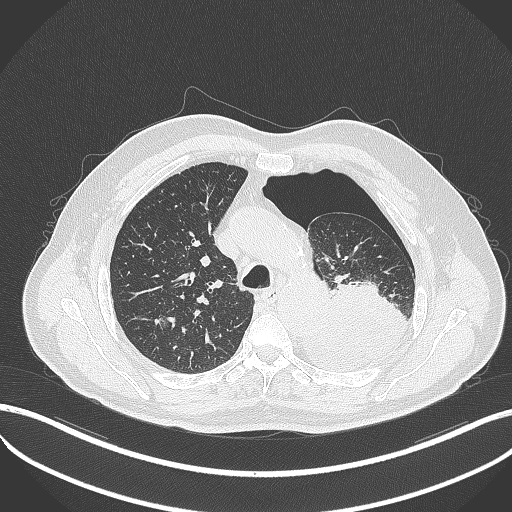
Chest CT, one axial slice. Slice 369 of 464 in the series (ordered by position). 120 kVp. Lung window (W 1500 / L -600 HU). 1 mm slice thickness. 512 × 512 image matrix, field of view 400 × 400 mm. Male patient, age 76 years. From the clinical record (not read from this slice): clinical TNM (as recorded): T3 N0 M1b.
Annotated regions visible in this slice (bounding box drawn by a radiologist):
- lung tumour (recorded histology: adenocarcinoma): bounding box [x1, y1, x2, y2] px = [294, 272, 412, 372]